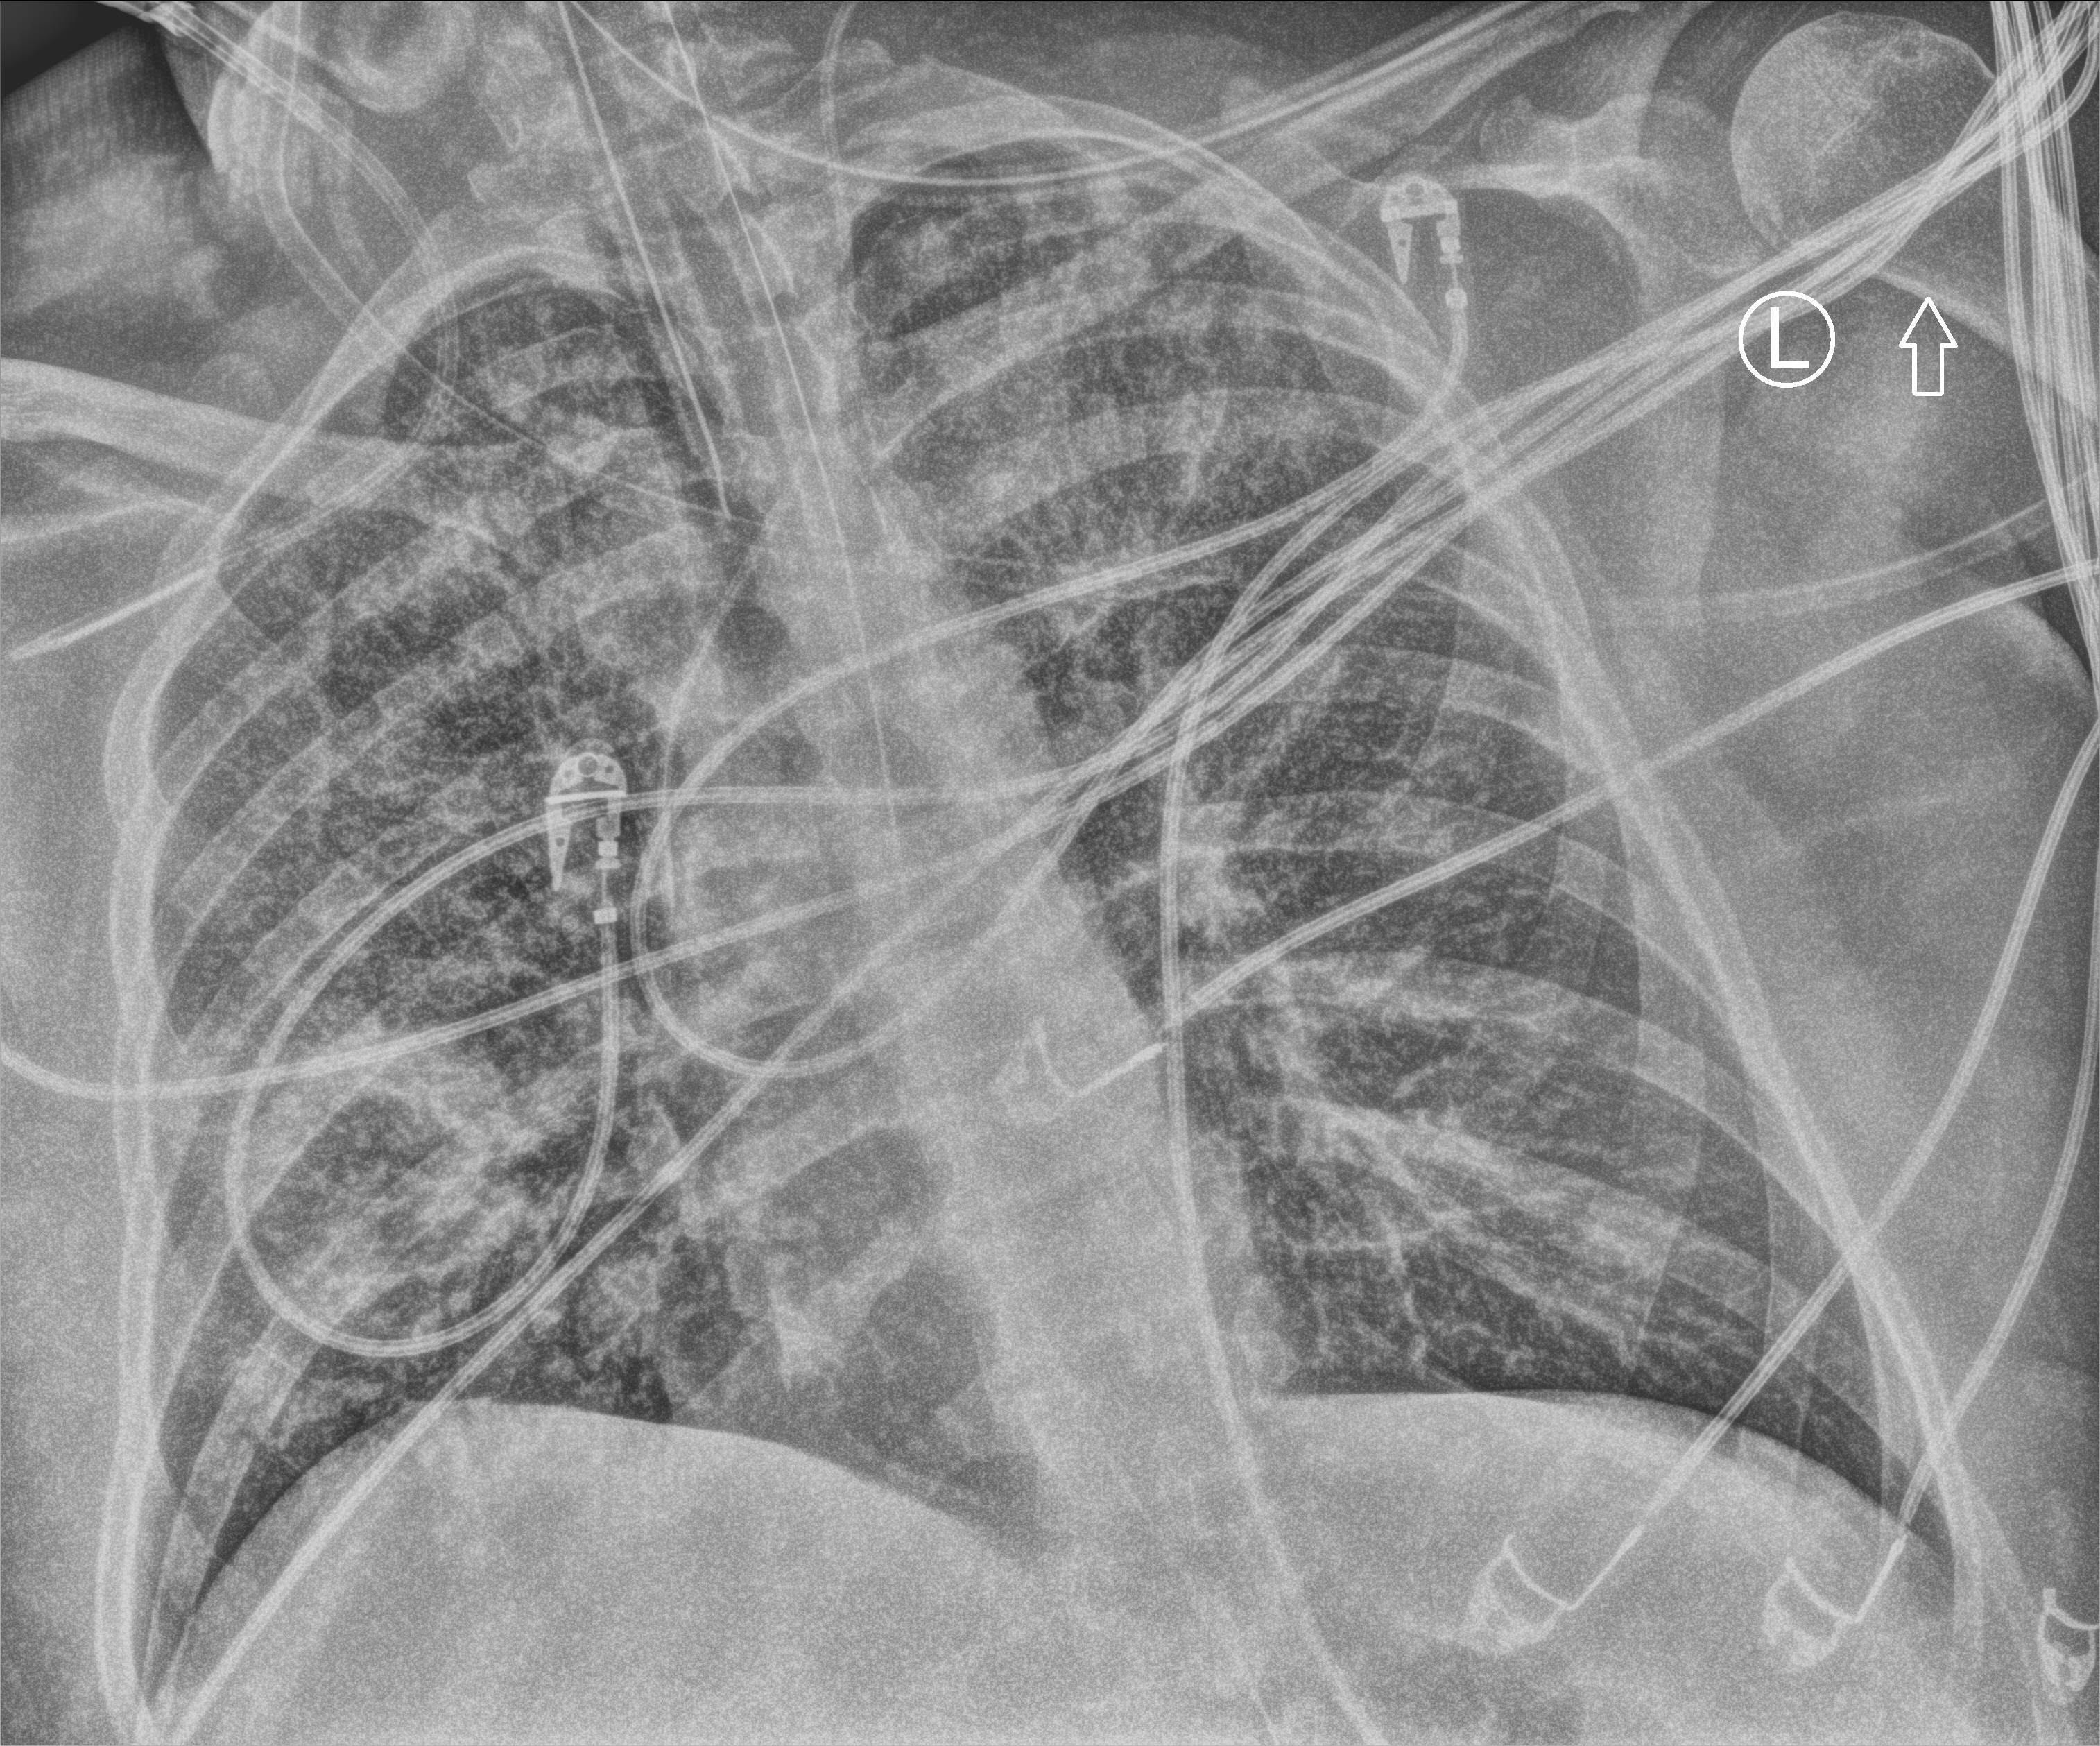
Bedside chest radiograph (computed radiography); anteroposterior (AP) projection. Patient hospitalised with COVID-19, aged 18–59 years.
Admission-level facts for this patient (not findings on this image; timing relative to this image not recorded):
- hypertension (admission record): no
- length of hospital stay: 16 days